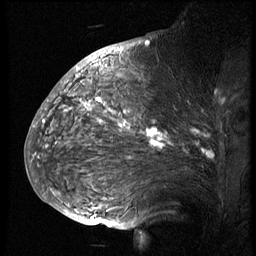
Breast MRI (dynamic contrast-enhanced), one sagittal slice. Position 41 of 74 along the scan axis. 3 images stored at this slice position (order not interpretable as contrast timing). 1.5 T. TE 4.2 ms, TR 8.9 ms. 2.5 mm slice thickness. 256 × 256 image matrix. Patient: female, 57 years. Case-level facts recorded for this patient, not image findings: setting: breast cancer imaged before/during neoadjuvant chemotherapy; receptor status: HER2-positive.
Annotated regions visible in this slice (semi-automatic segmentation, software-assisted and operator-edited):
- analysis volume of interest (the breast-tissue region the enhancement analysis was run in; not a lesion): bounding box <51,67,249,173> (left, top, right, bottom; pixels)
- tumour enhancement mask (voxels above the 140 % enhancement threshold inside the analysis volume of interest): <66,99,212,157>